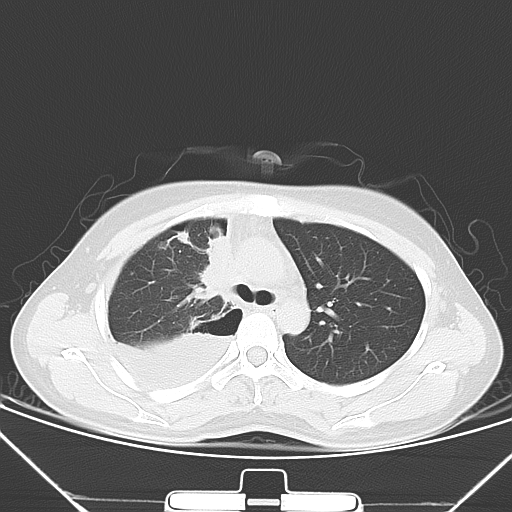
Chest CT, one axial slice. Slice 44 of 62 in the series (ordered by position). 120 kVp. Lung window (W 1500 / L -600 HU). 5 mm slice thickness. 512 × 512 image matrix. Female patient, age 28 years. From the clinical record (not read from this slice): clinical TNM (as recorded): T2 N0 M1a.
Structures marked on this image (bounding box drawn by a radiologist):
- lung tumour (recorded histology: adenocarcinoma): box from (x=185, y=227) to (x=236, y=309) px